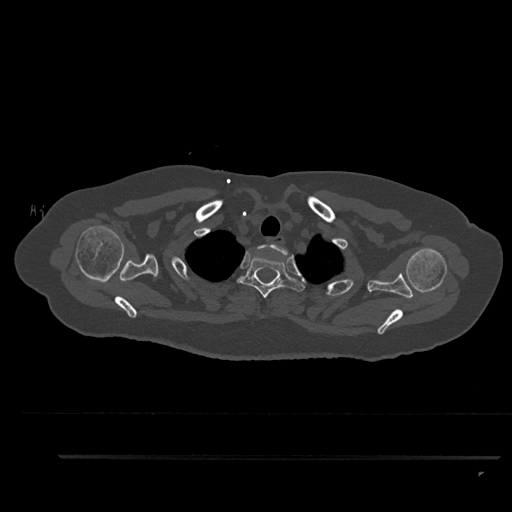
CT including the spine, one axial slice. Slice 729 of 797 in the series (ordered by position). Reconstruction kernel Br40s/3. 120 kVp. Bone window (W 1800 / L 400 HU). 0.5 mm slice thickness. 512 × 512 image matrix, field of view 408 × 408 mm. Female patient, age 44 years. Case-level facts recorded for this patient, not image findings: primary cancer: renal; vertebrae with lytic lesions (as recorded): L1.
Annotated regions visible in this slice (semi-automatically segmented with operator editing):
- T1 vertebra: bounding box [x1, y1, x2, y2] px = [253, 244, 288, 257]
- T2 vertebra: [236, 256, 305, 298]